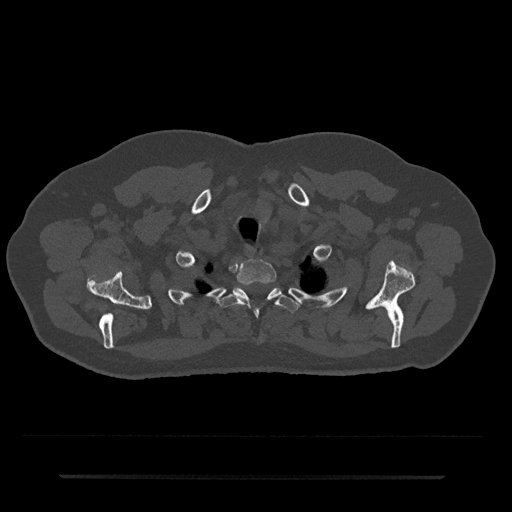
CT including the spine, one axial slice; position 619 of 797 along the scan axis; bone window (W 1800 / L 400 HU); 512 × 512 image matrix, field of view 437 × 437 mm. Patient: male, 69 years. From the clinical record (not read from this slice): primary cancer: prostate.
Structures marked on this image (semi-automatic segmentation, software-assisted and operator-edited):
- T1 vertebra: bounding box <237,259,277,286> (left, top, right, bottom; pixels)
- T2 vertebra: <220,288,299,342>